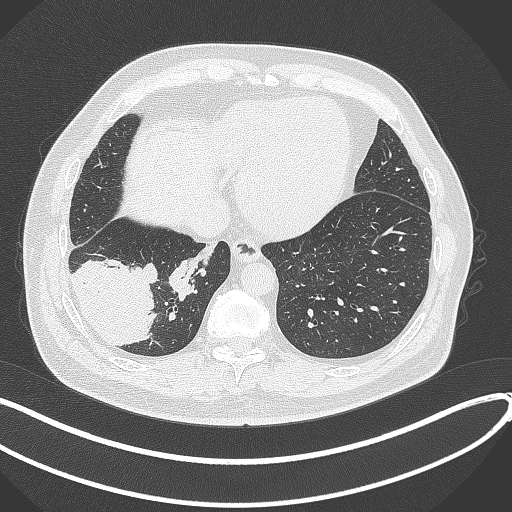
Chest CT, one axial slice; position 90 of 360 along the scan axis; 120 kVp; lung window (W 1500 / L -600 HU); 512 × 512 image matrix, field of view 400 × 400 mm. Male patient, age 59 years.
Outlined on this slice (bounding box drawn by a radiologist):
- lung tumour (recorded histology: adenocarcinoma): bounding box <70,252,158,348> (left, top, right, bottom; pixels)